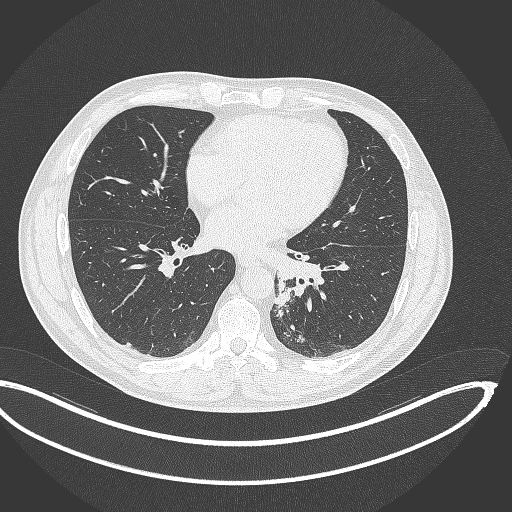
Chest CT, one axial slice. Position 146 of 362 along the scan axis. 120 kVp. Lung window (W 1500 / L -600 HU). 1 mm slice thickness. 512 × 512 image matrix. Patient: male, 50 years. From the clinical record (not read from this slice): clinical TNM (as recorded): T2a N3 M0.
Outlined on this slice (rectangle marked by the reading radiologist):
- lung tumour (recorded histology: squamous cell carcinoma): box from (x=270, y=276) to (x=295, y=315) px